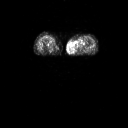
FDG PET of an extremity soft-tissue mass (from a PET/CT study), one axial slice; position 9 of 91 along the scan axis; 3.27 mm slice thickness; 128 × 128 image matrix, field of view 700 × 700 mm. Patient: female, 74 years. Case-level facts recorded for this patient, not image findings: histological type: pleomorphic leiomyosarcoma; grade: high; site of the primary tumour: left thigh.
Structures marked on this image (expert contour drawn on MRI and transferred to this co-registered scan by the dataset authors):
- gross tumour volume including surrounding oedema: box from (x=72, y=38) to (x=87, y=51) px